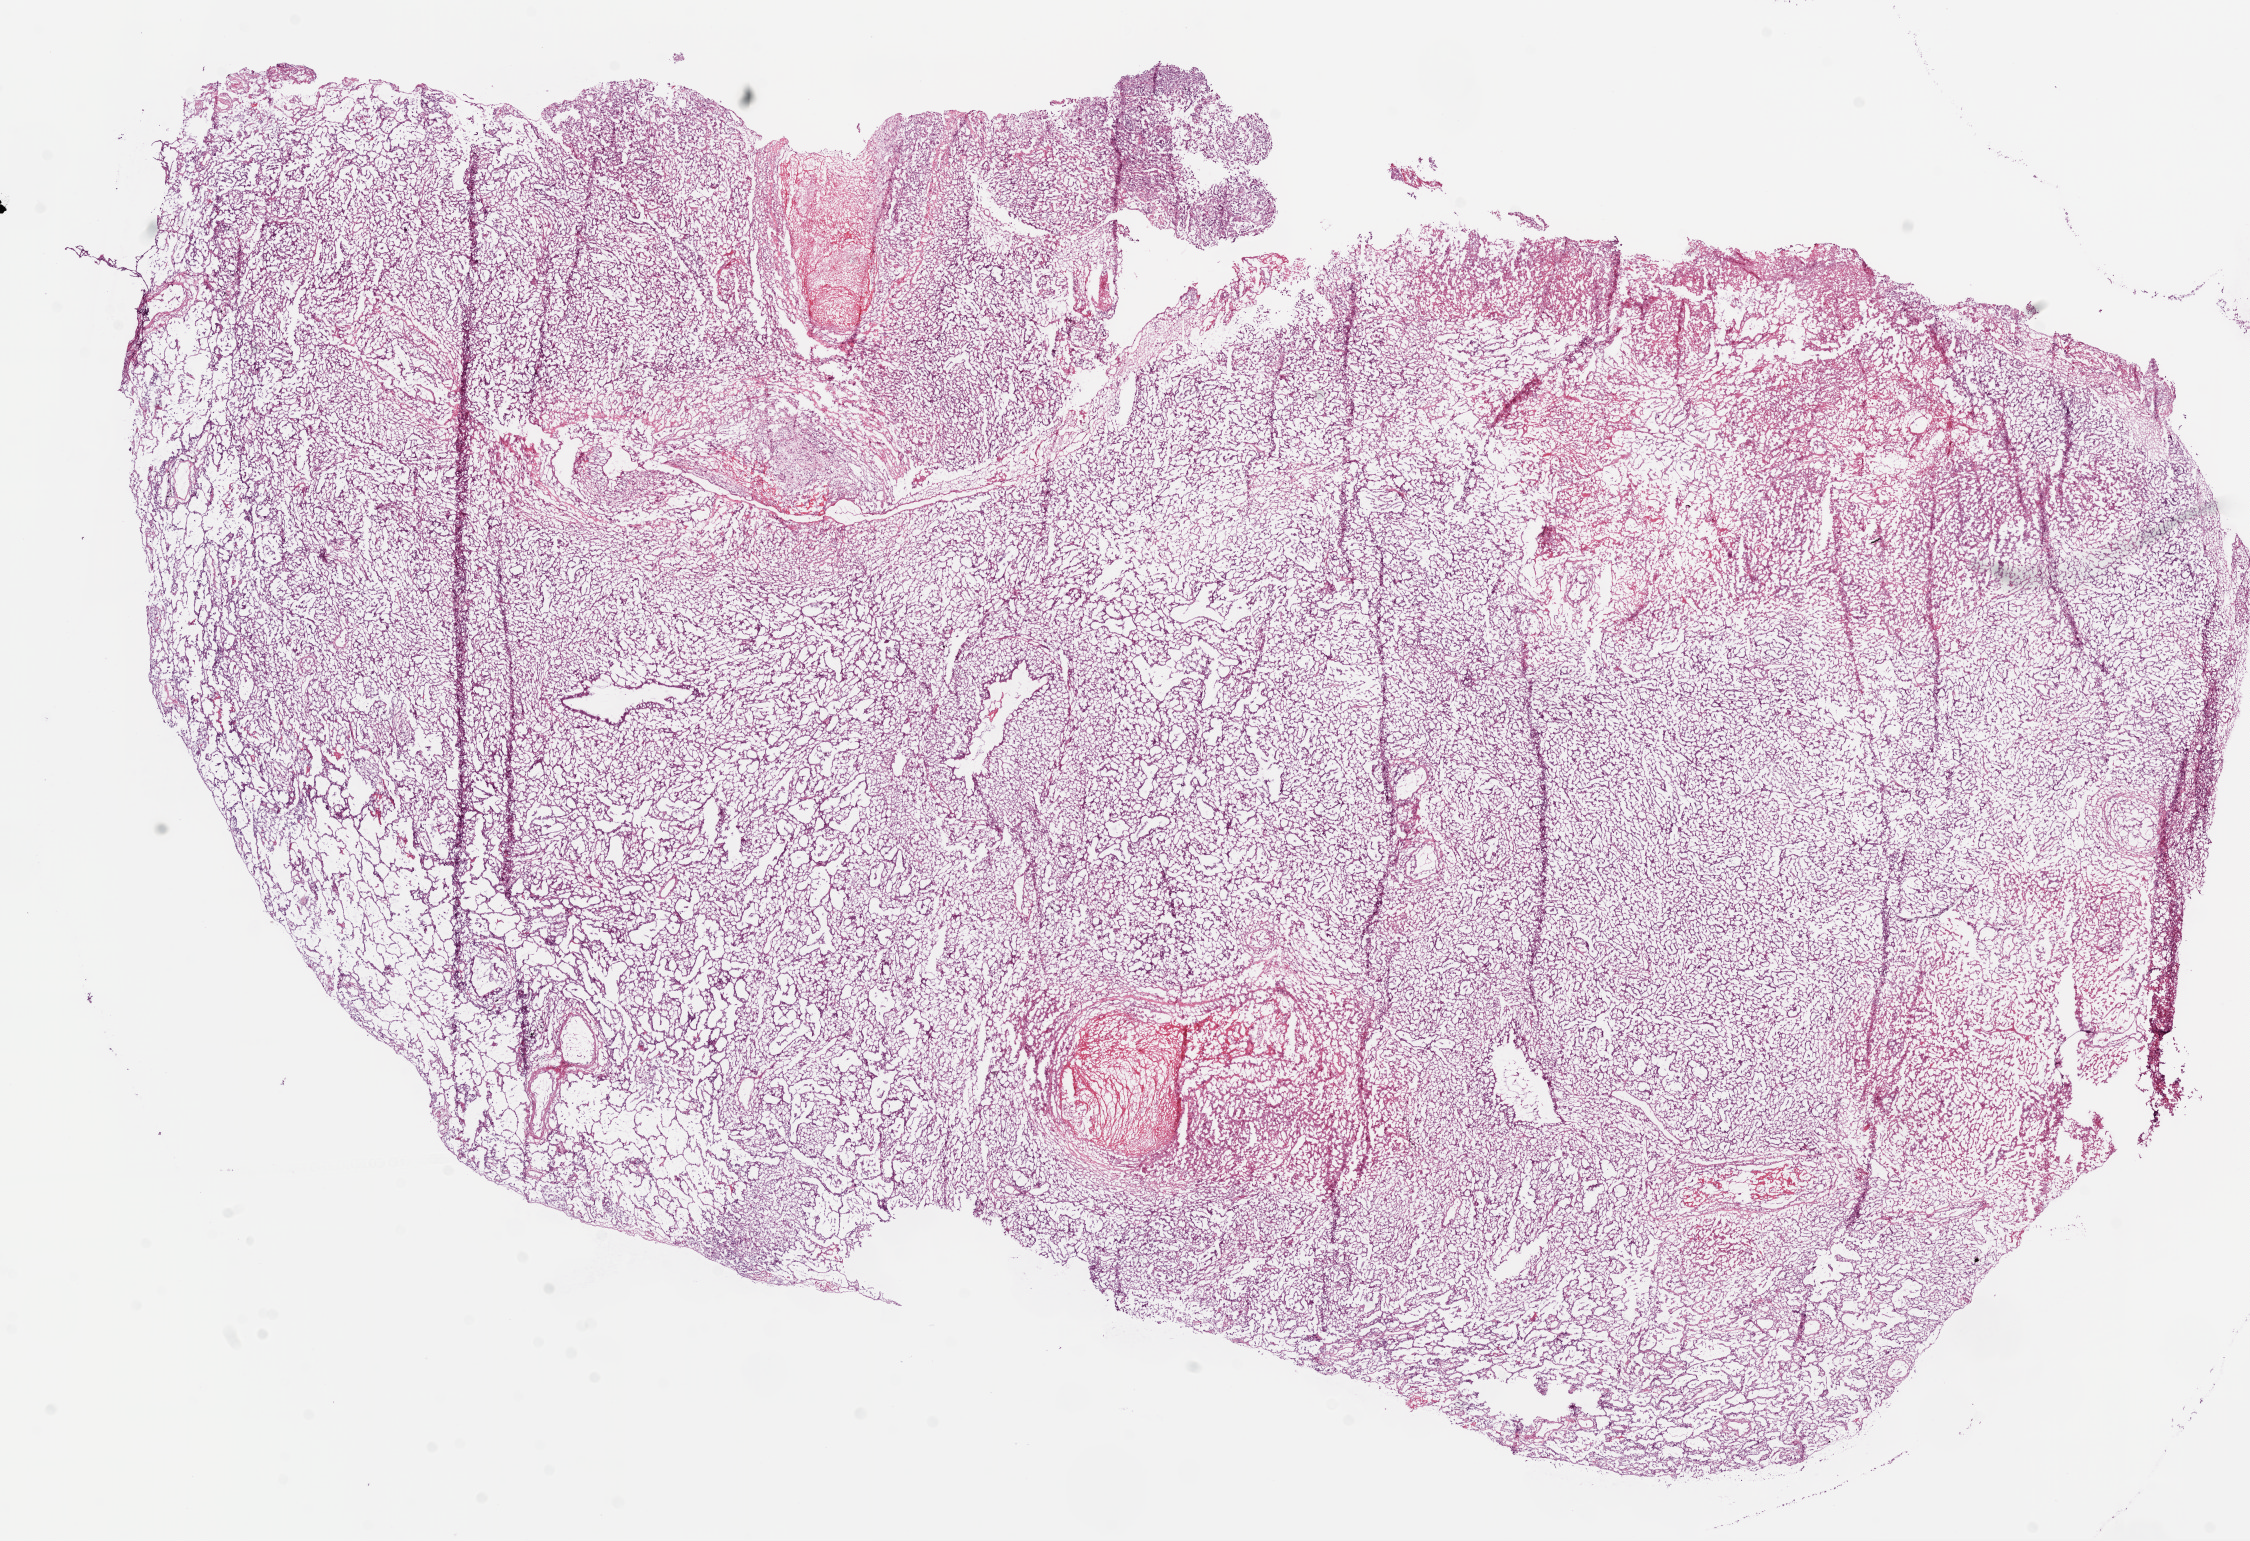
H&E-stained whole-slide image, whole scanned area (about 18.1 x 12.4 mm, from a 20x scan) shown as a low-resolution overview. Frozen section. Lung, primary tumour sample. Female patient; age at initial diagnosis 72 years. Slide review estimates, as recorded: tumour cells 80%, tumour nuclei 80%, normal cells 15%, stromal cells 5%, necrosis 0%.
Pathologic diagnosis: Adenocarcinoma, NOS (lower lobe, lung). AJCC pathologic stage: IIIB (5th edition).